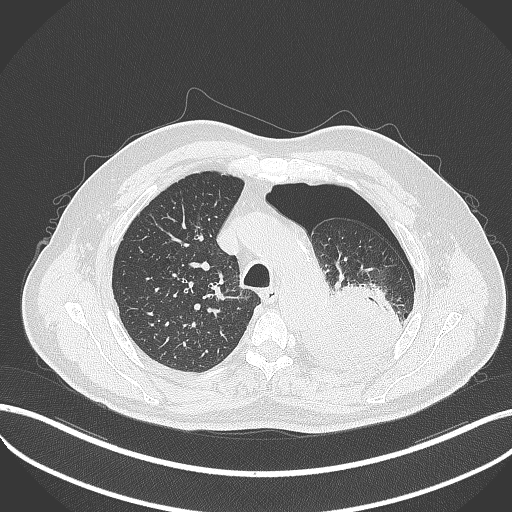
Chest CT, one axial slice. Slice 381 of 464 in the series (ordered by position). Reconstruction kernel B70f. 120 kVp. Lung window (W 1500 / L -600 HU). 1 mm slice thickness. 512 × 512 image matrix. Patient: male, 76 years. From the clinical record (not read from this slice): clinical TNM (as recorded): T3 N0 M1b.
Outlined on this slice (rectangle marked by the reading radiologist):
- lung tumour (recorded histology: adenocarcinoma): bounding box [x1, y1, x2, y2] px = [298, 278, 402, 374]